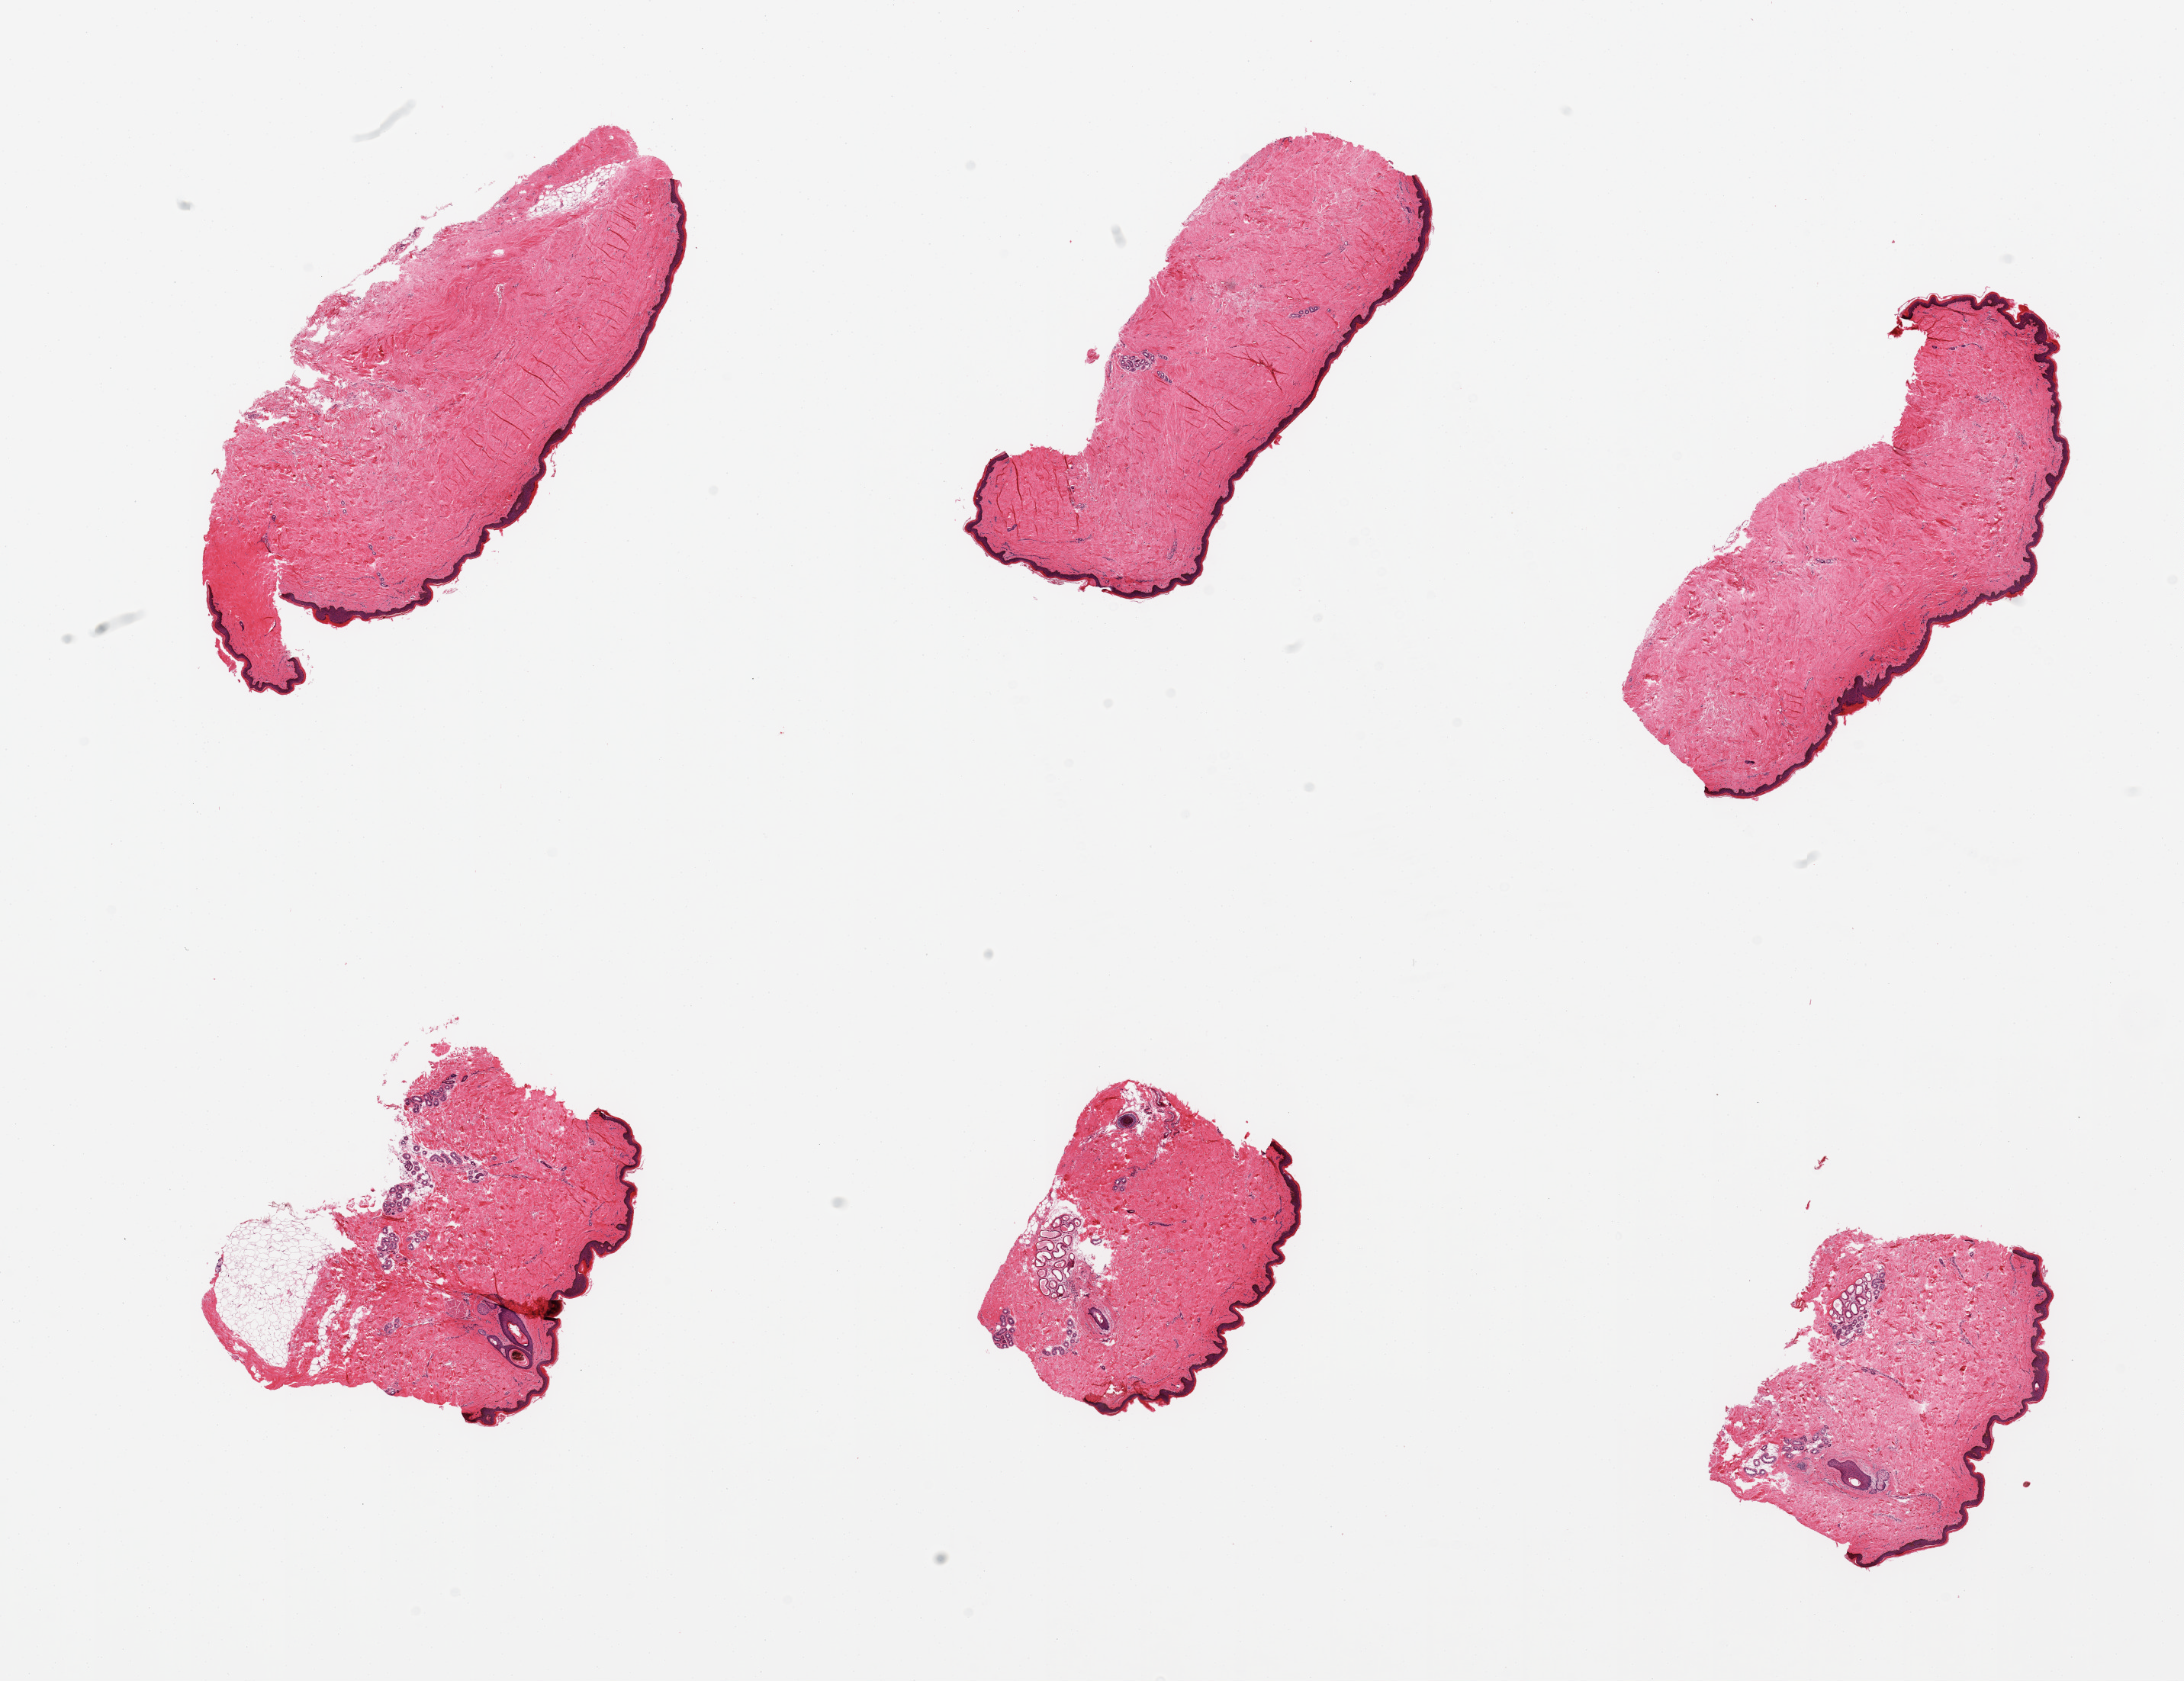
Hematoxylin and eosin (H&E) whole-slide image, whole scanned area (about 22.6 x 17.4 mm, slide scanned at 20x) shown as a low-resolution overview, PAXgene-fixed, paraffin-embedded tissue, section of skin of suprapubic region (target tissue), donor tissue sample.
Reviewer comment on this tissue sample: 6 pieces; essentially well trimmed except one piece with attached ~1mm external fat.